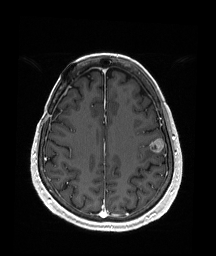
Brain MRI from a brain-tumour surgery series, one axial slice; T1-weighted post-contrast; 216 × 256 image matrix. From the clinical record (not read from this slice): histopathology: Metastatic Malignant Melanoma; tumour location: Left Frontal.
Annotated regions visible in this slice (outlined manually by an expert reader):
- tumour: box from (x=149, y=138) to (x=164, y=153) px